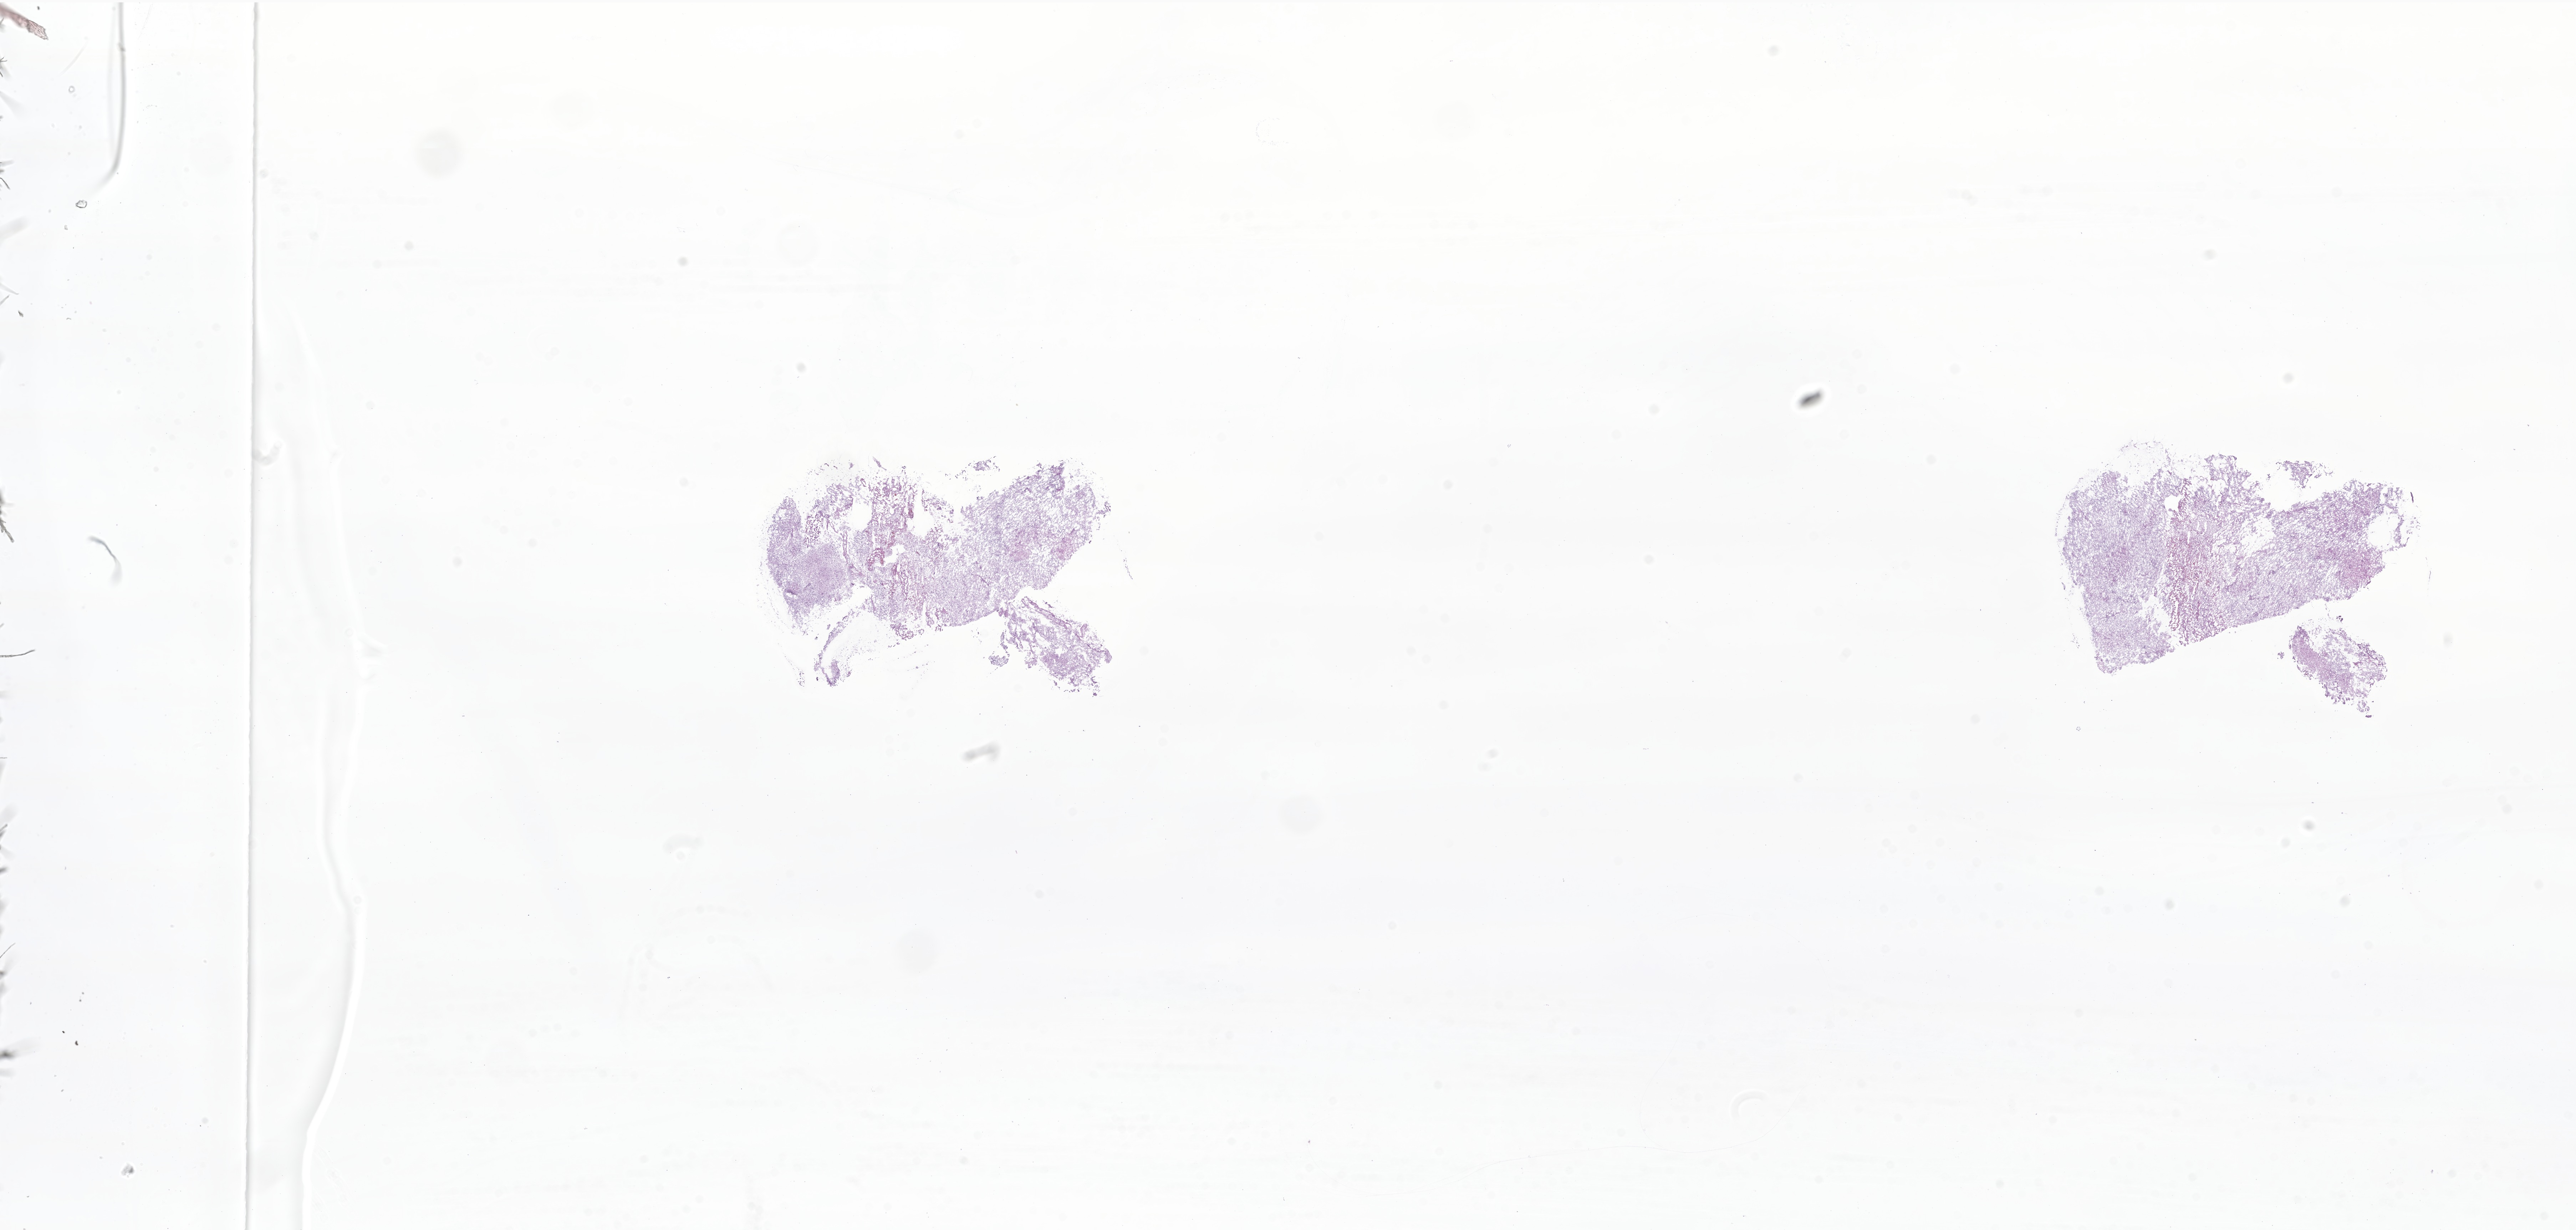
Digitized hematoxylin and eosin (H&E)-stained section of tumor tissue from the brain, shown as a low-resolution overview of the whole scanned area (about 30.4 x 14.5 mm). Cryosection (OCT / tissue freezing medium). Female patient, age 48 months (4 years).
Recorded diagnosis: Pilocytic astrocytoma.